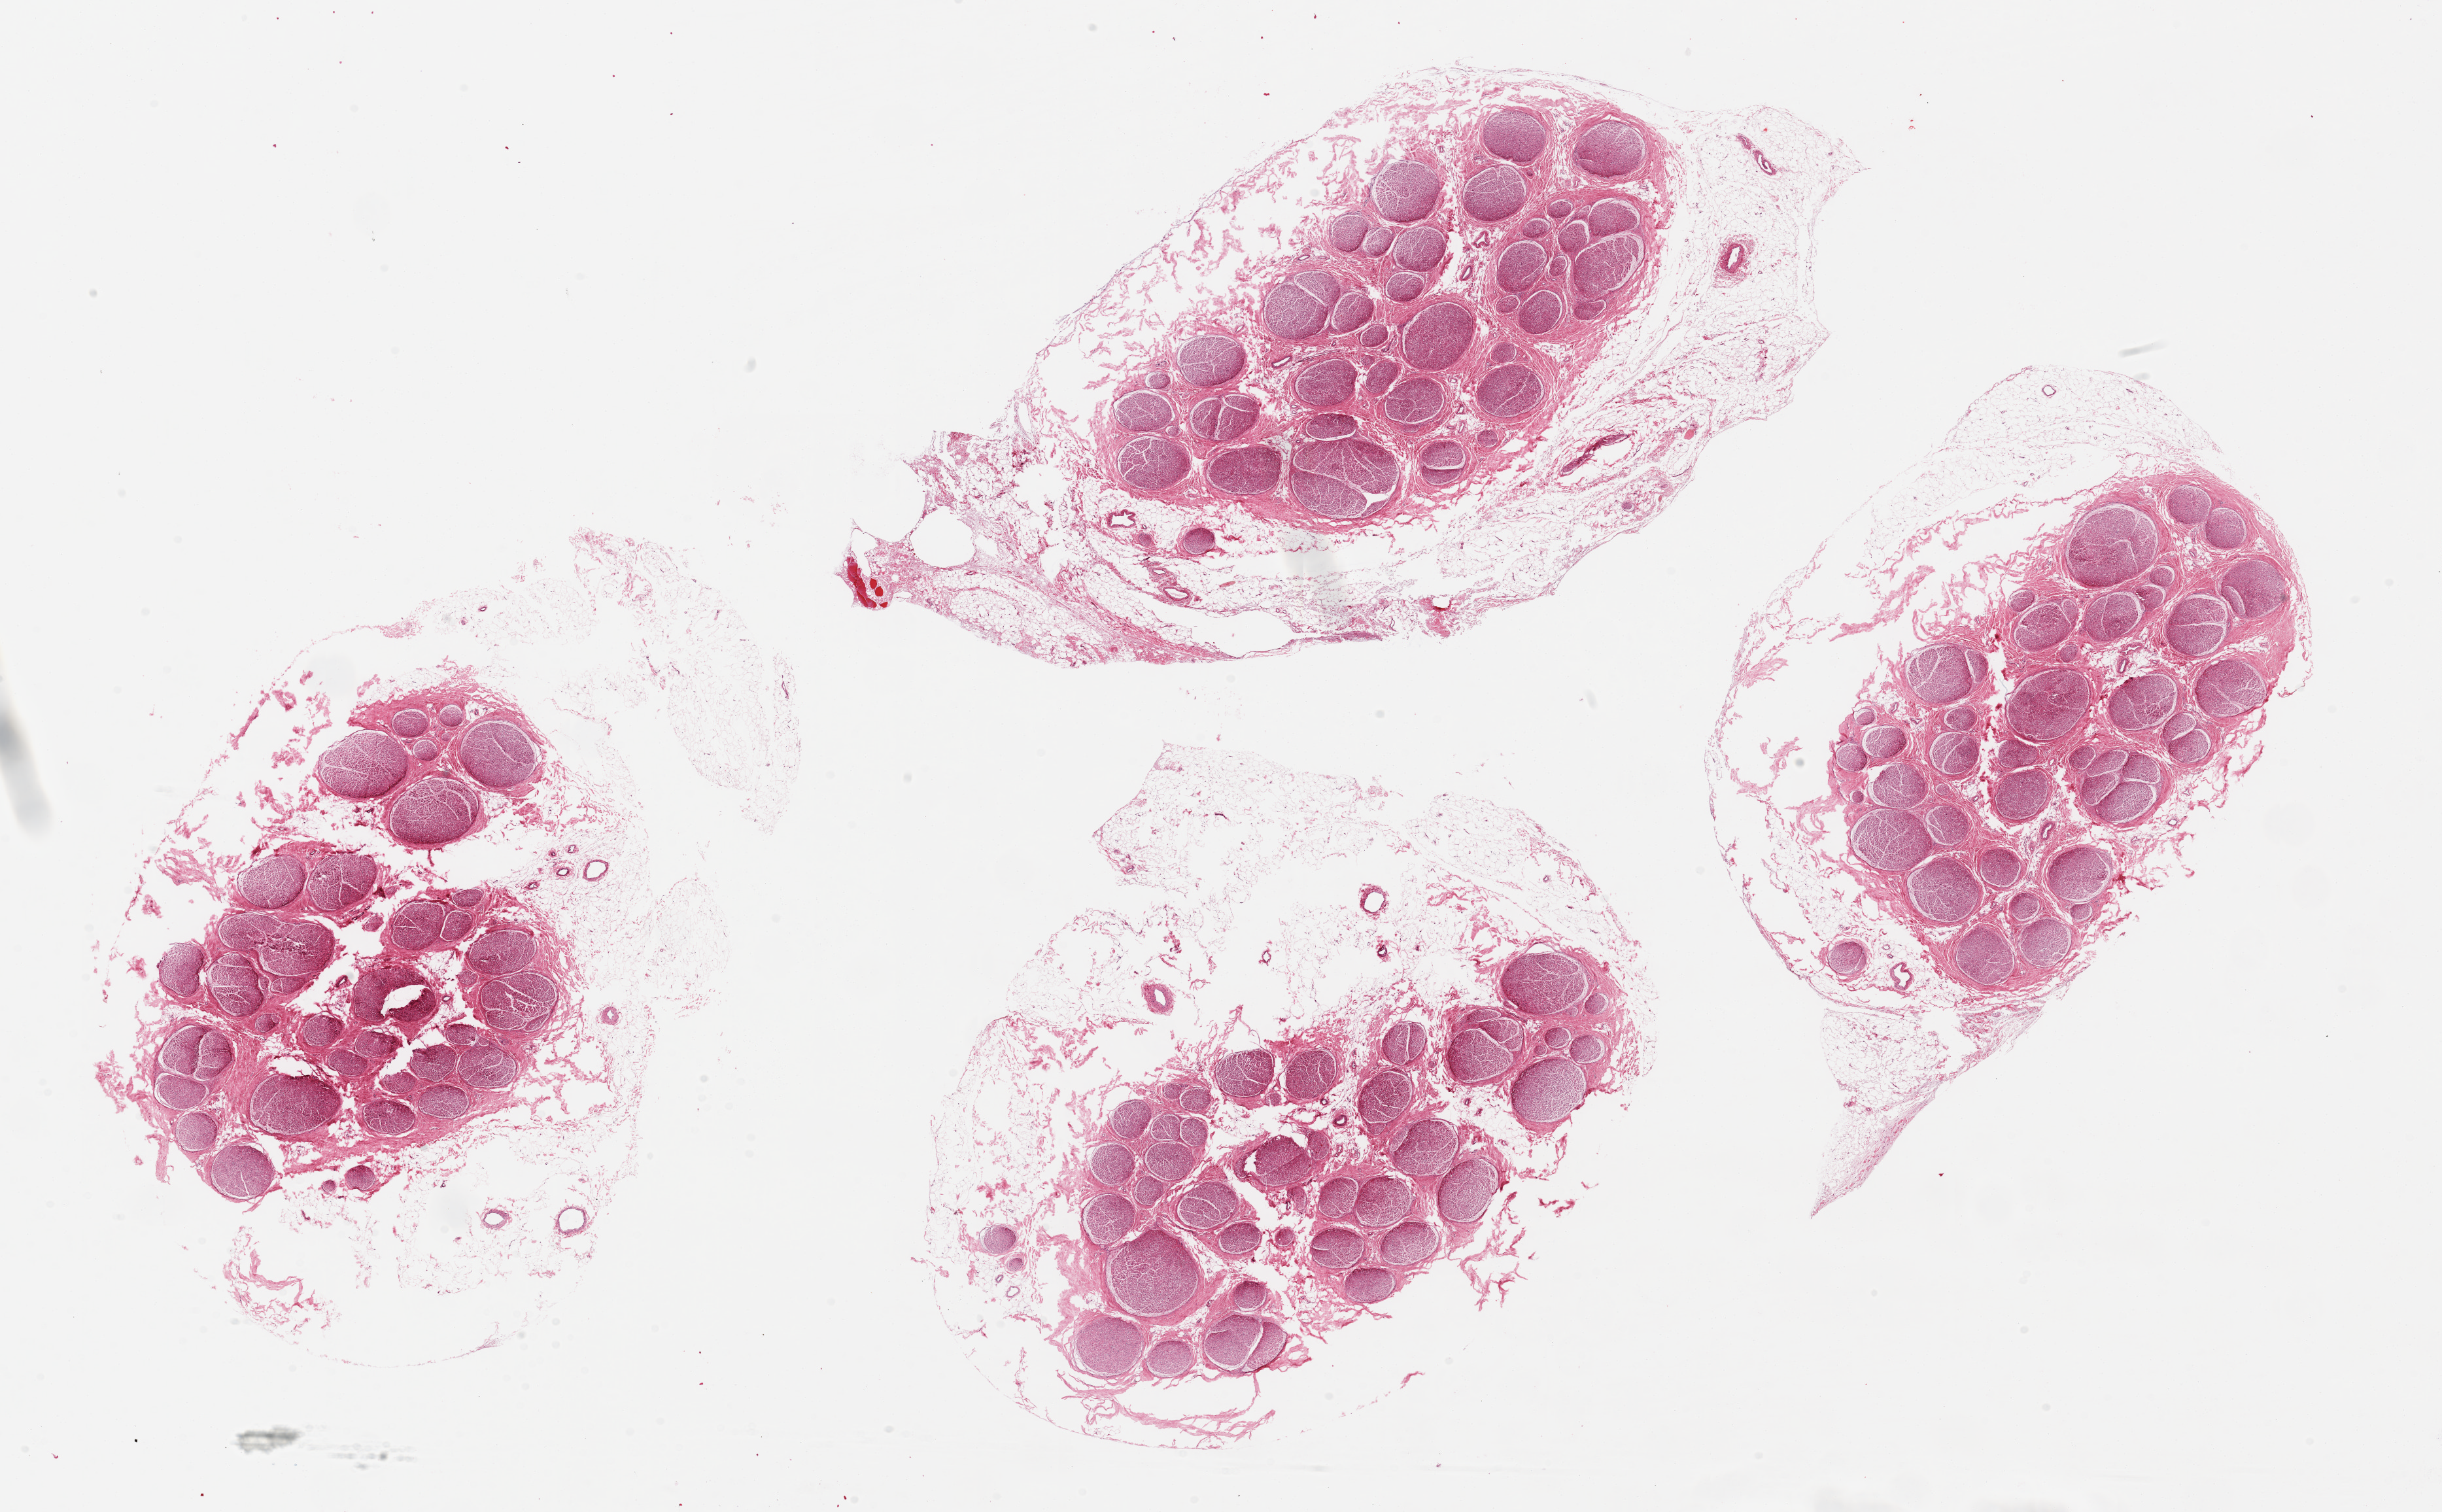
Whole-slide image, haematoxylin and eosin stain — a low-resolution overview of the entire scanned area, about 29.5 x 18.3 mm (slide scanned at 20x). PAXgene-fixed paraffin-embedded (PFPE) section. Section of tibial nerve (target tissue). Donor tissue sample. Donor sex: male.
Pathologist's review note for this sample: 4 pieces, up to 11x6 mm; all encased in abundant extraneous adipose, up to 4 mm thick.